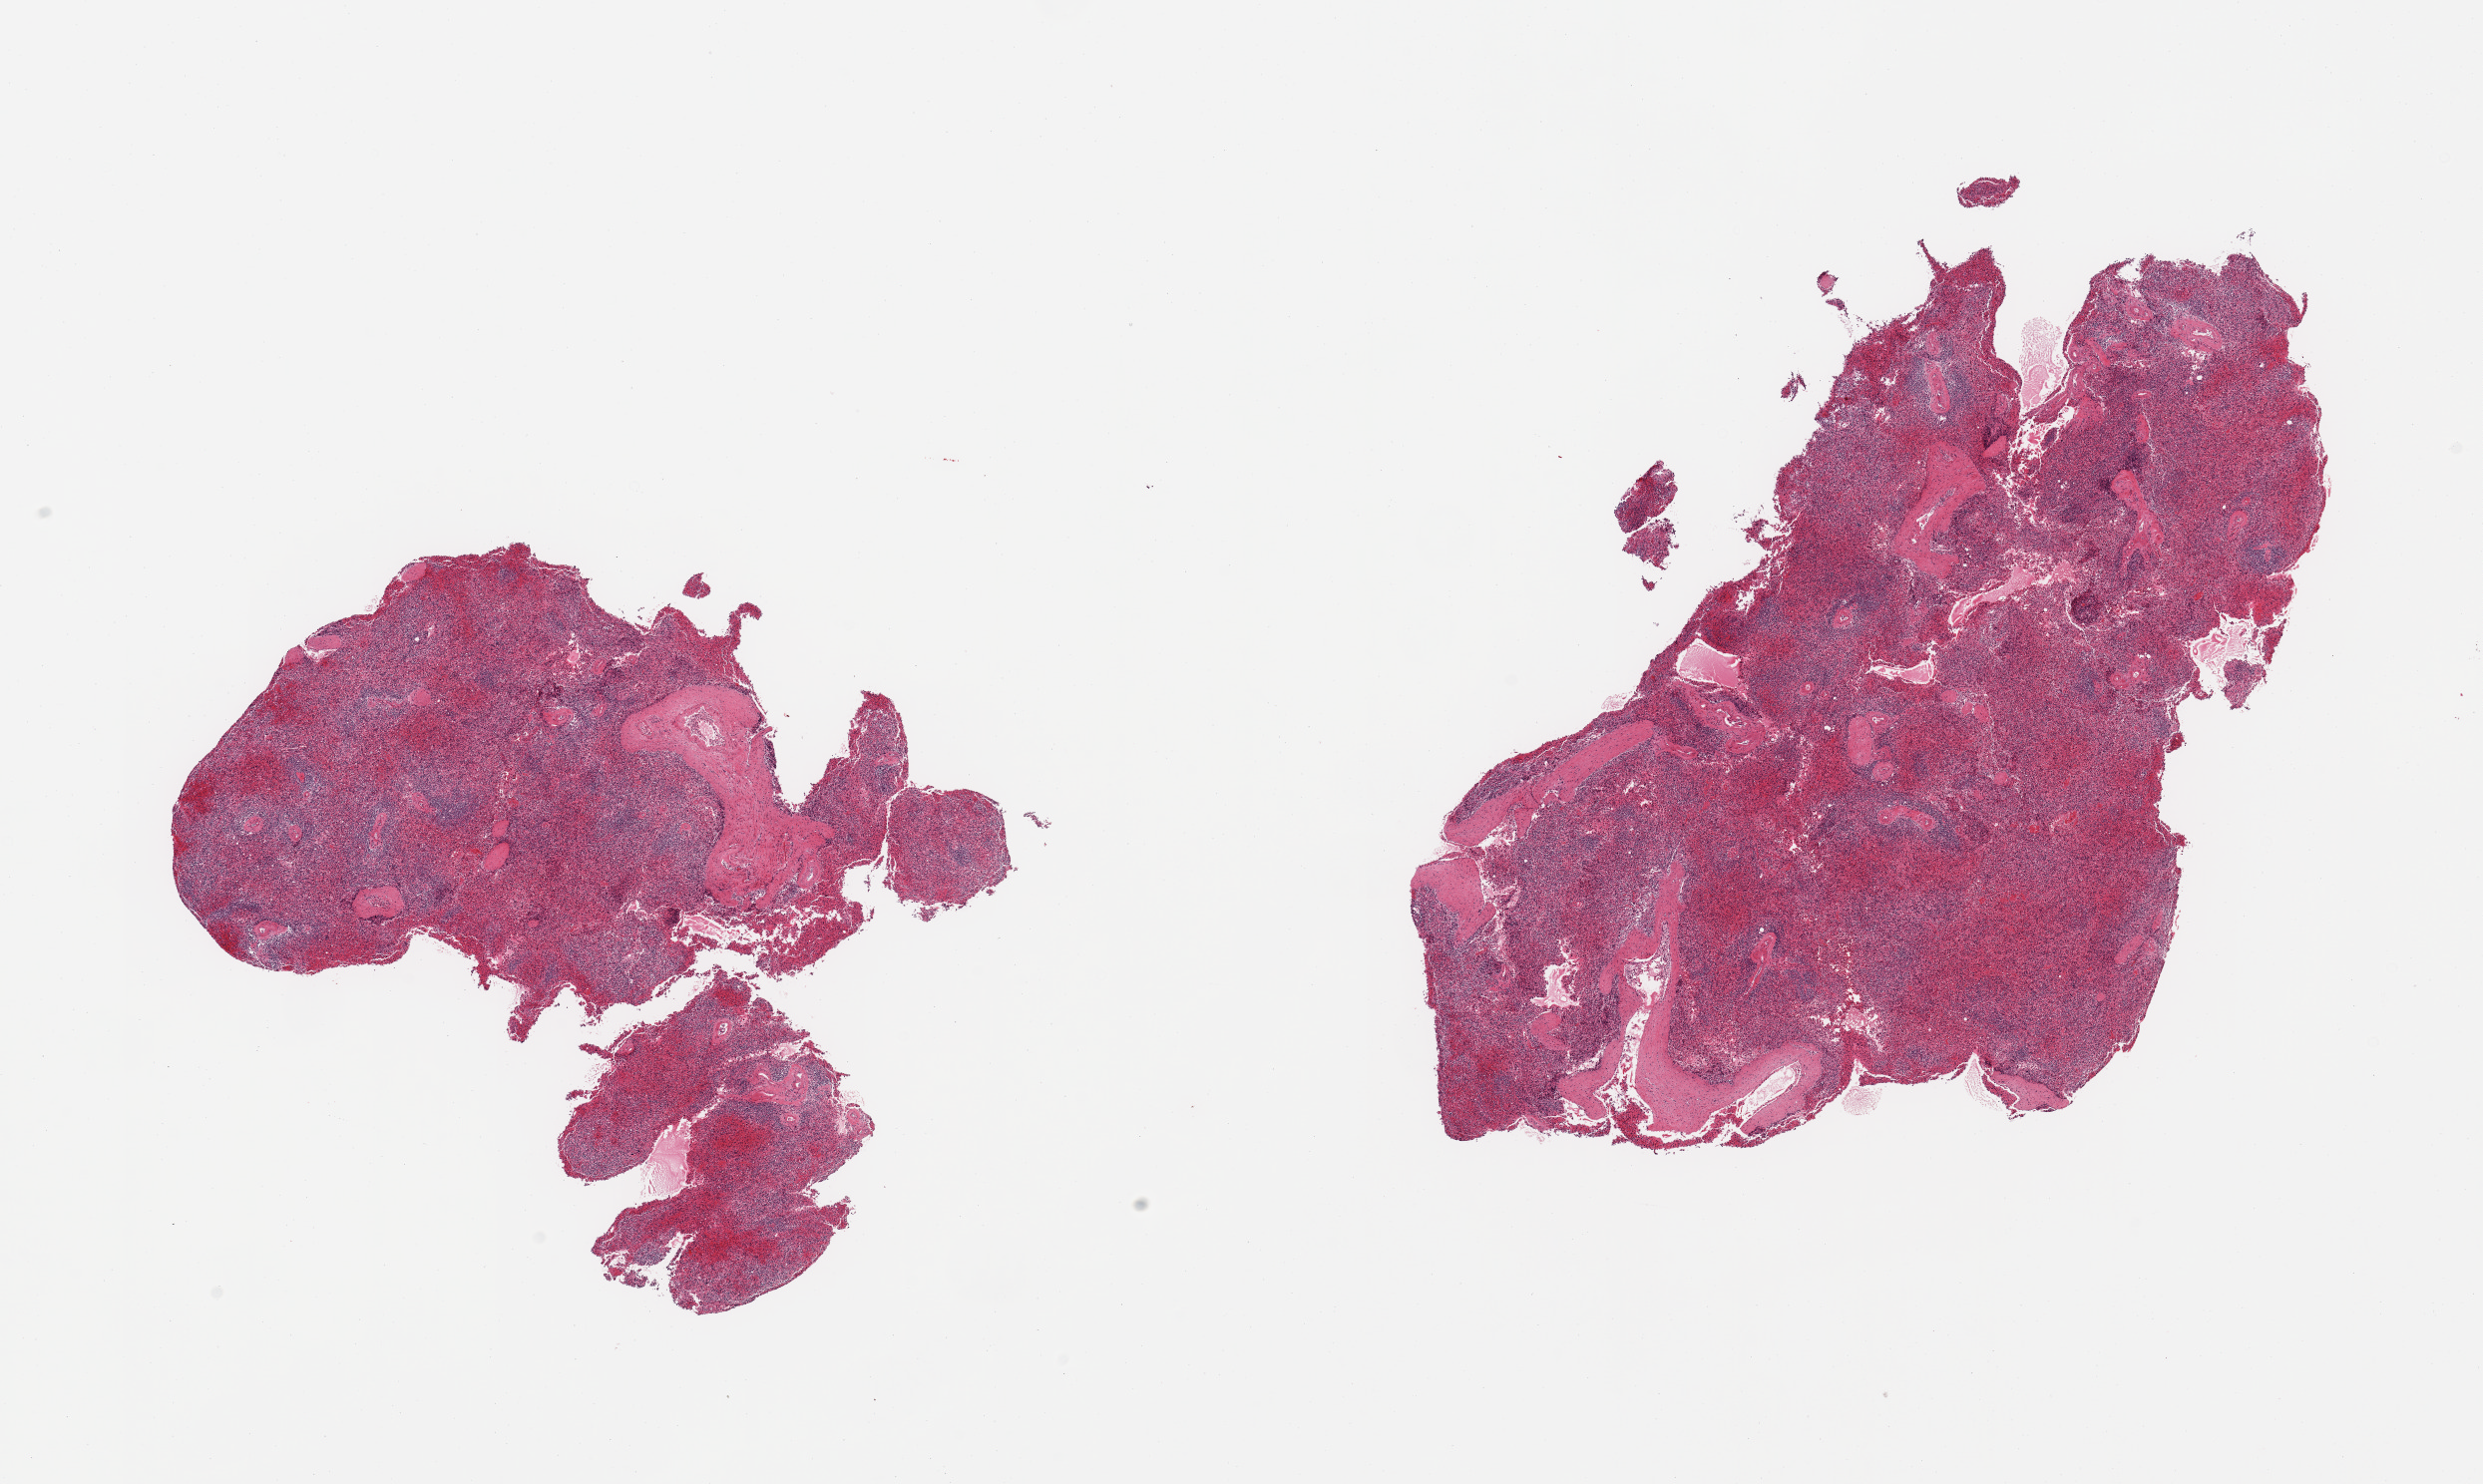
Haematoxylin and eosin whole-slide image, a low-resolution overview of the entire scanned area, about 19.7 x 11.8 mm, PAXgene-fixed paraffin-embedded (PFPE) section, sampled site (target tissue): spleen, tissue donor sample. Donor: female.
- pathologist's review note for this sample: 2 pieces; moderate congestion; fragmented tissue